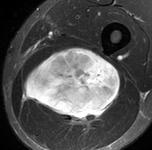
MRI of an extremity soft-tissue mass, one axial slice. Slice 61 of 90 in the series (ordered by position). STIR. MR volume resampled by the dataset authors to the PET/CT grid (not the native acquisition matrix). 152 × 150 image matrix, field of view 148 × 146 mm. Male patient. From the clinical record (not read from this slice): histological type: undifferentiated pleomorphic liposarcoma; grade: high; site of the primary tumour: left thigh.
Annotated regions visible in this slice (expert contour drawn on MRI and transferred to this co-registered scan by the dataset authors):
- gross tumour volume including surrounding oedema: bounding box [x1, y1, x2, y2] px = [20, 46, 122, 127]
- gross tumour volume (mass): [20, 46, 122, 124]